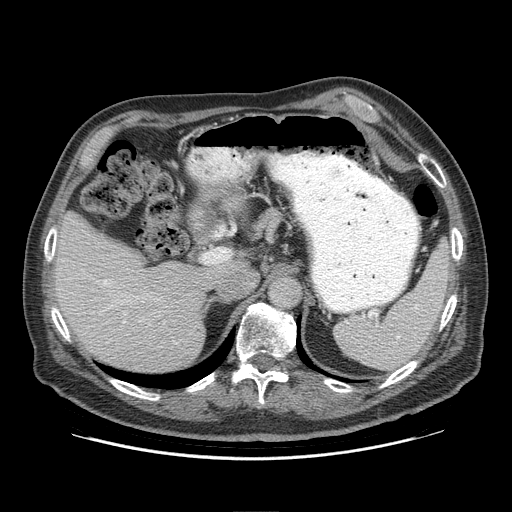
Contrast-enhanced abdominal CT (liver protocol), one axial slice. Position 60 of 95 along the scan axis. Reconstruction kernel STANDARD. 140 kVp. Soft-tissue window (W 400 / L 40 HU). 2.5 mm slice thickness. 512 × 512 image matrix, field of view 400 × 400 mm. Case-level facts recorded for this patient, not image findings: diagnosis: hepatocellular carcinoma (patient treated with transarterial chemoembolisation; whether this scan precedes or follows treatment is not stated here); TNM stage (as recorded): Stage-IVB; Child-Pugh class: A; tumour nodularity: uninodular.
Structures marked on this image (semi-automatic segmentation, software-assisted and operator-edited):
- liver parenchyma outside the tumour (the mass and vessels are separate outlines, so this box may not span the whole liver): box from (x=54, y=212) to (x=210, y=372) px
- liver vessels: (x=104, y=280)–(x=125, y=323)